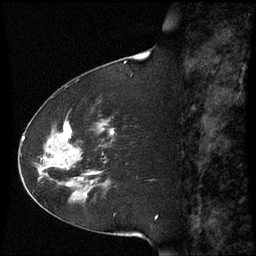
Breast MRI (dynamic contrast-enhanced), one sagittal slice. Slice 22 of 60 in the series (ordered by position). Dynamic contrast-enhanced series, image 2 of 3 at this slice position (ordered by acquisition). 1.5 T. TE 4.2 ms, TR 8.9 ms. 2.3 mm slice thickness. 256 × 256 image matrix, field of view 210 × 210 mm. Female patient, age 51 years. Case-level facts recorded for this patient, not image findings: setting: breast cancer imaged before/during neoadjuvant chemotherapy; receptor status: HR-positive, HER2-negative.
Outlined on this slice (semi-automatic segmentation, software-assisted and operator-edited):
- analysis volume of interest (the breast-tissue region the enhancement analysis was run in; not a lesion): bounding box <50,117,115,187> (left, top, right, bottom; pixels)
- tumour enhancement mask (voxels above the 70 % enhancement threshold inside the analysis volume of interest): <50,123,114,162>